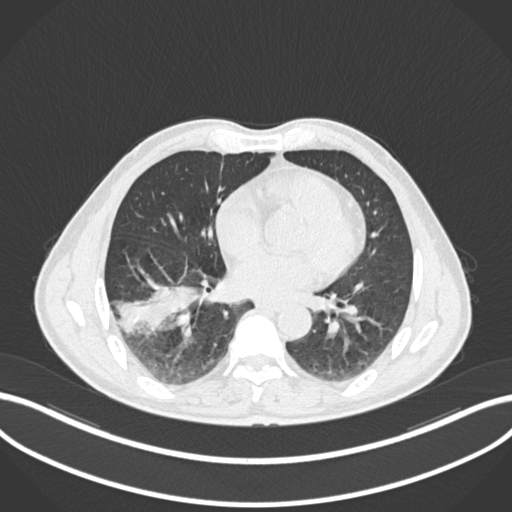
Chest CT, one axial slice; slice 79 of 208 in the series (ordered by position); reconstruction kernel B30f; lung window (W 1500 / L -600 HU); 1 mm slice thickness; 512 × 512 image matrix, field of view 400 × 400 mm. Patient: male, 58 years. From the clinical record (not read from this slice): clinical TNM (as recorded): T3 N0 M0.
Structures marked on this image (rectangle marked by the reading radiologist):
- lung tumour (recorded histology: squamous cell carcinoma): bounding box [x1, y1, x2, y2] px = [107, 276, 203, 339]